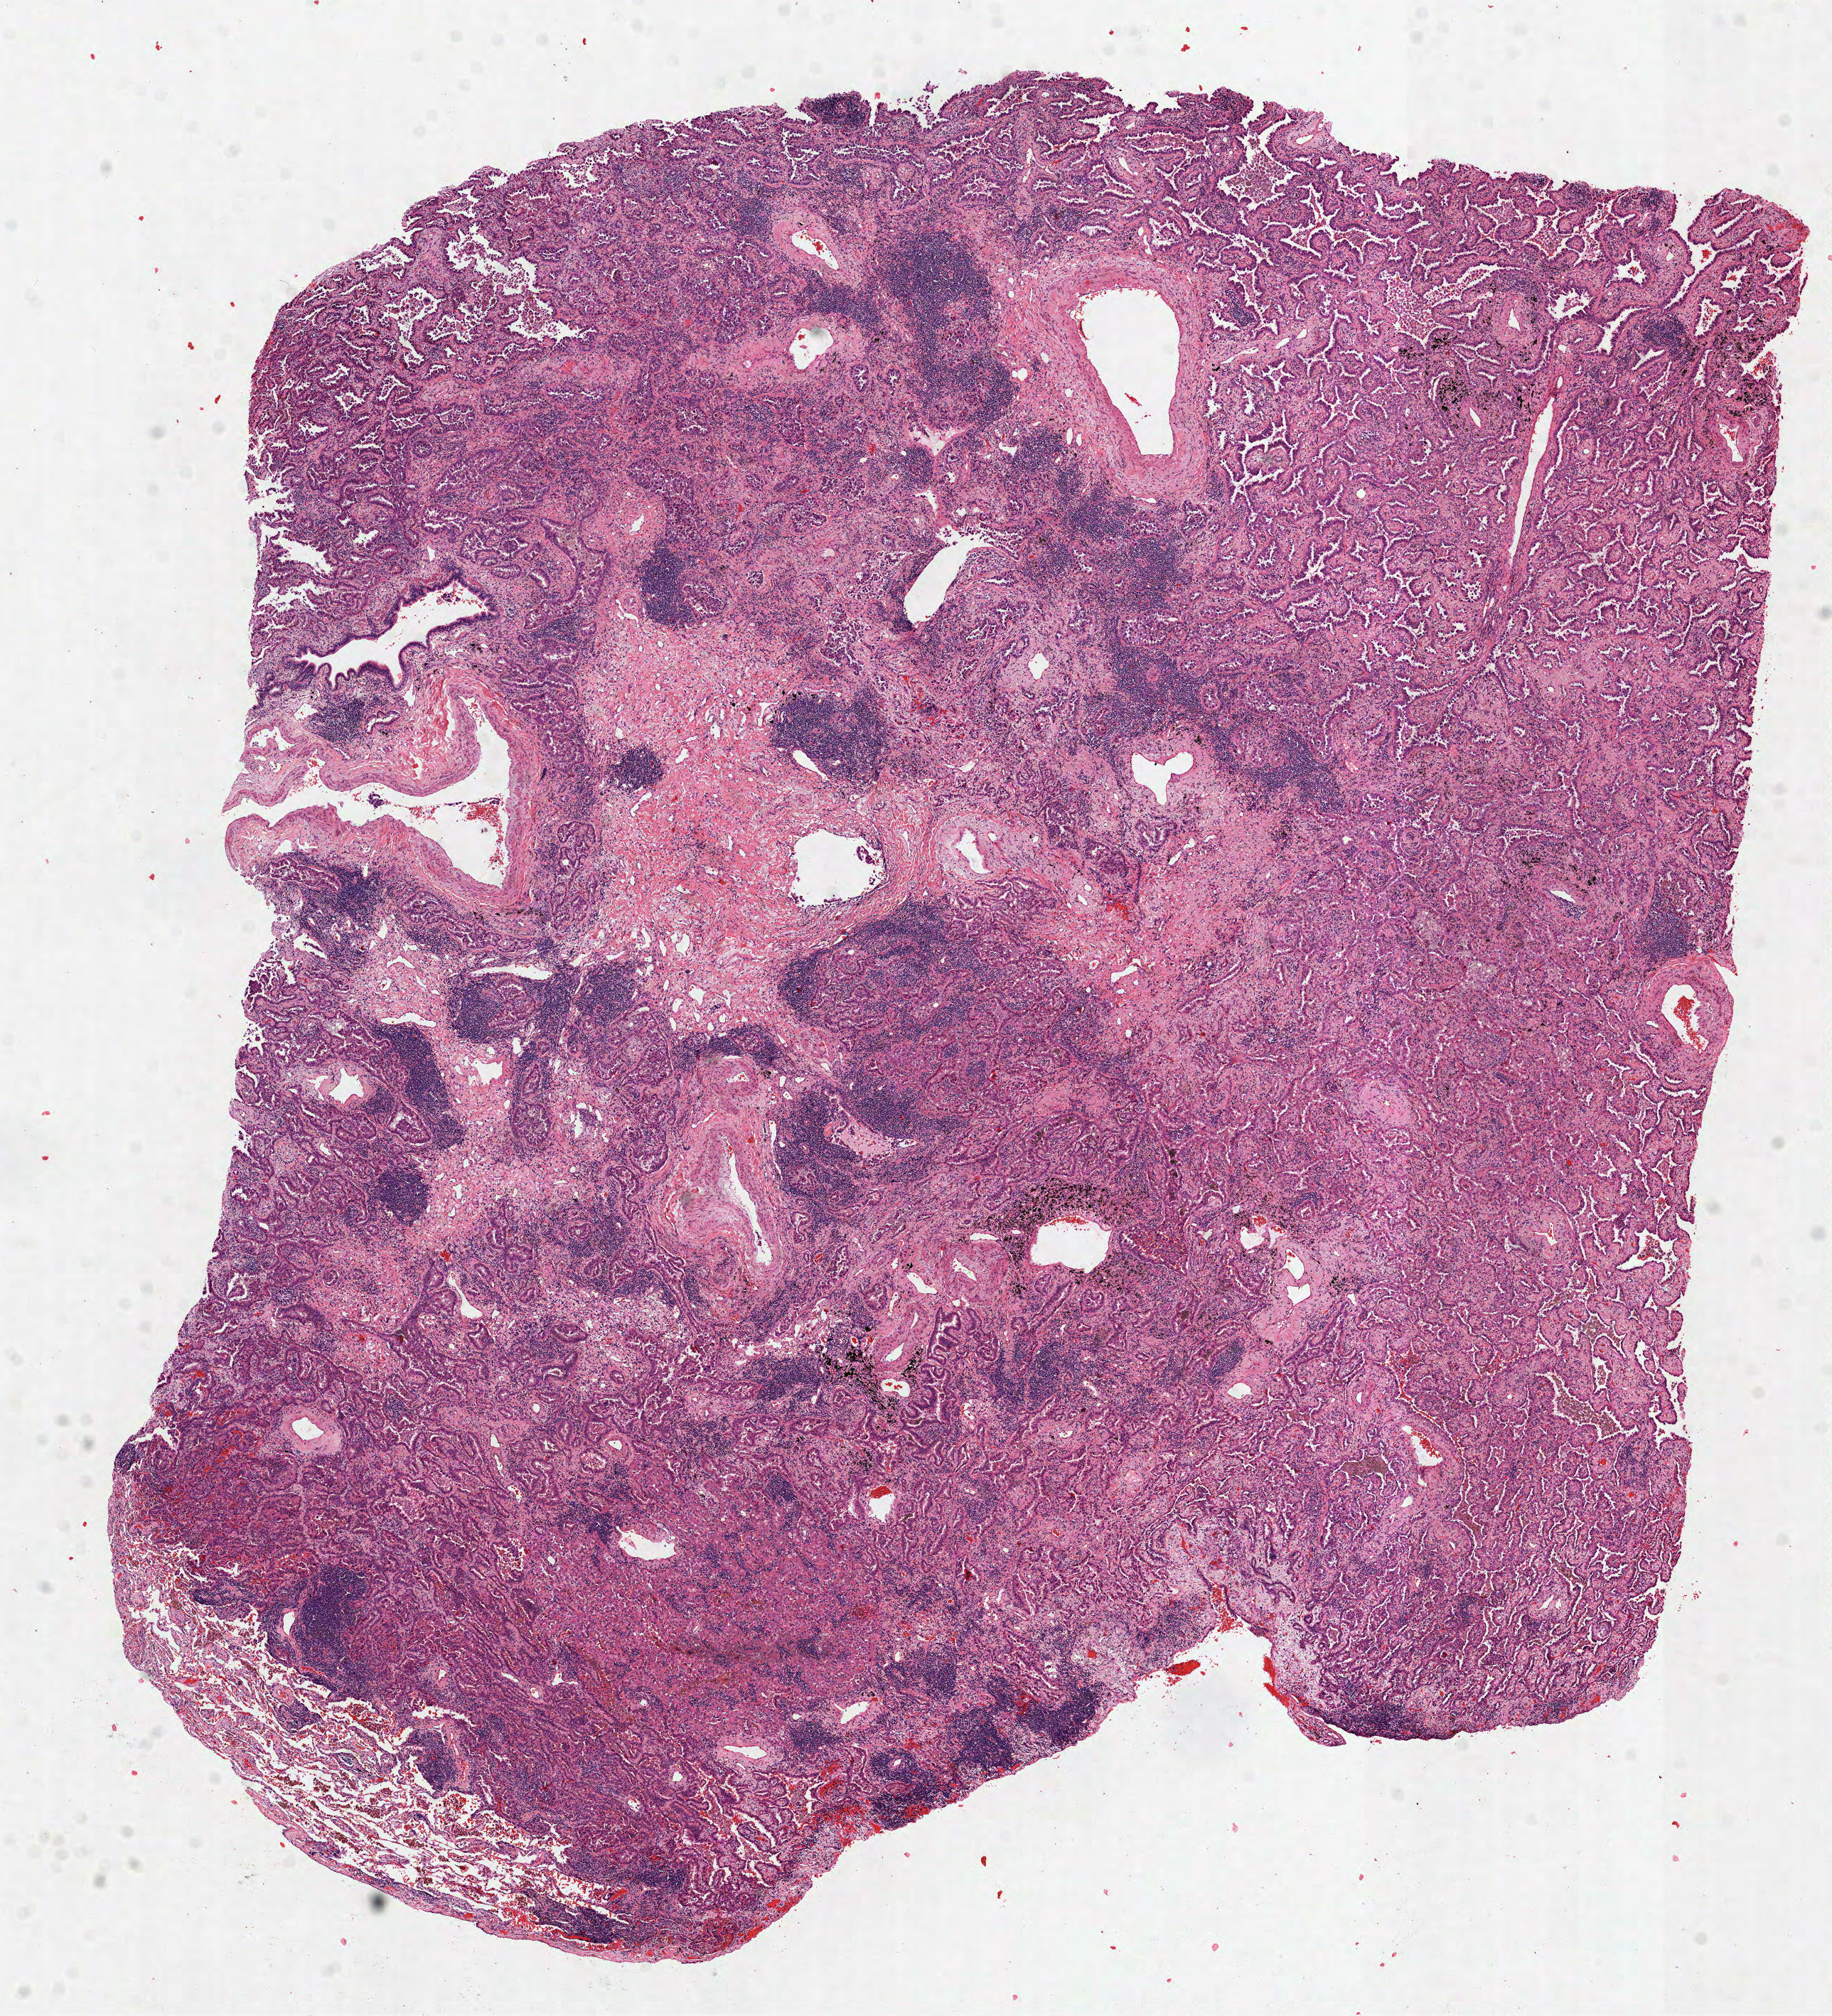
Whole-slide histology image, H&E, low-resolution overview of the scanned area, about 10.4 x 11.4 mm; frozen section from the top of the tissue portion; lung, primary tumour sample. Female, age 73 years at initial diagnosis. Slide review estimates, as recorded: tumour cells 65%, tumour nuclei 60%, normal cells 5%, stromal cells 30%, necrosis 0%.
Laterality: left. TNM: T2a N1 M0. Histologic diagnosis: Adenocarcinoma, NOS (upper lobe, lung). AJCC pathologic stage: IIA (7th edition).